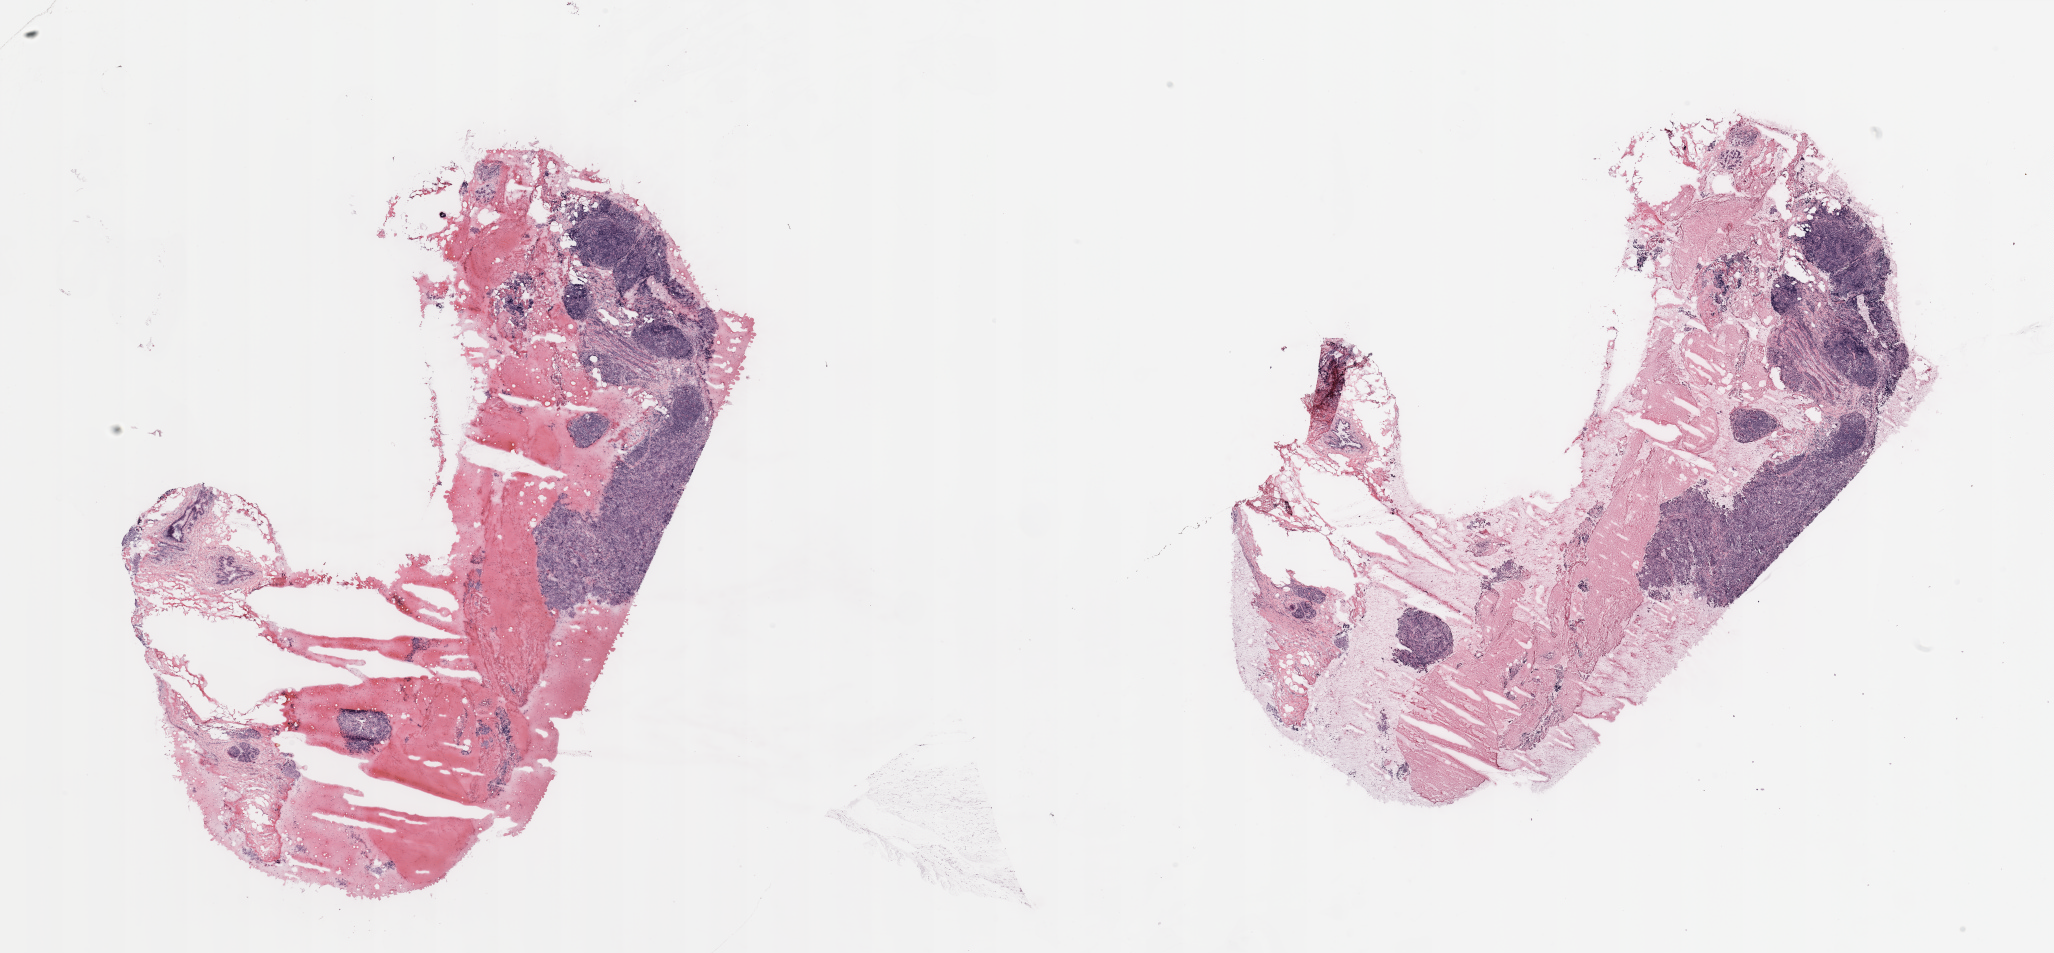
H&E whole-slide image, whole scanned area (about 32.5 x 15.1 mm, slide scanned at 20x) shown as a low-resolution overview. 48-year-old female patient.
- specimen: breast, tumour tissue